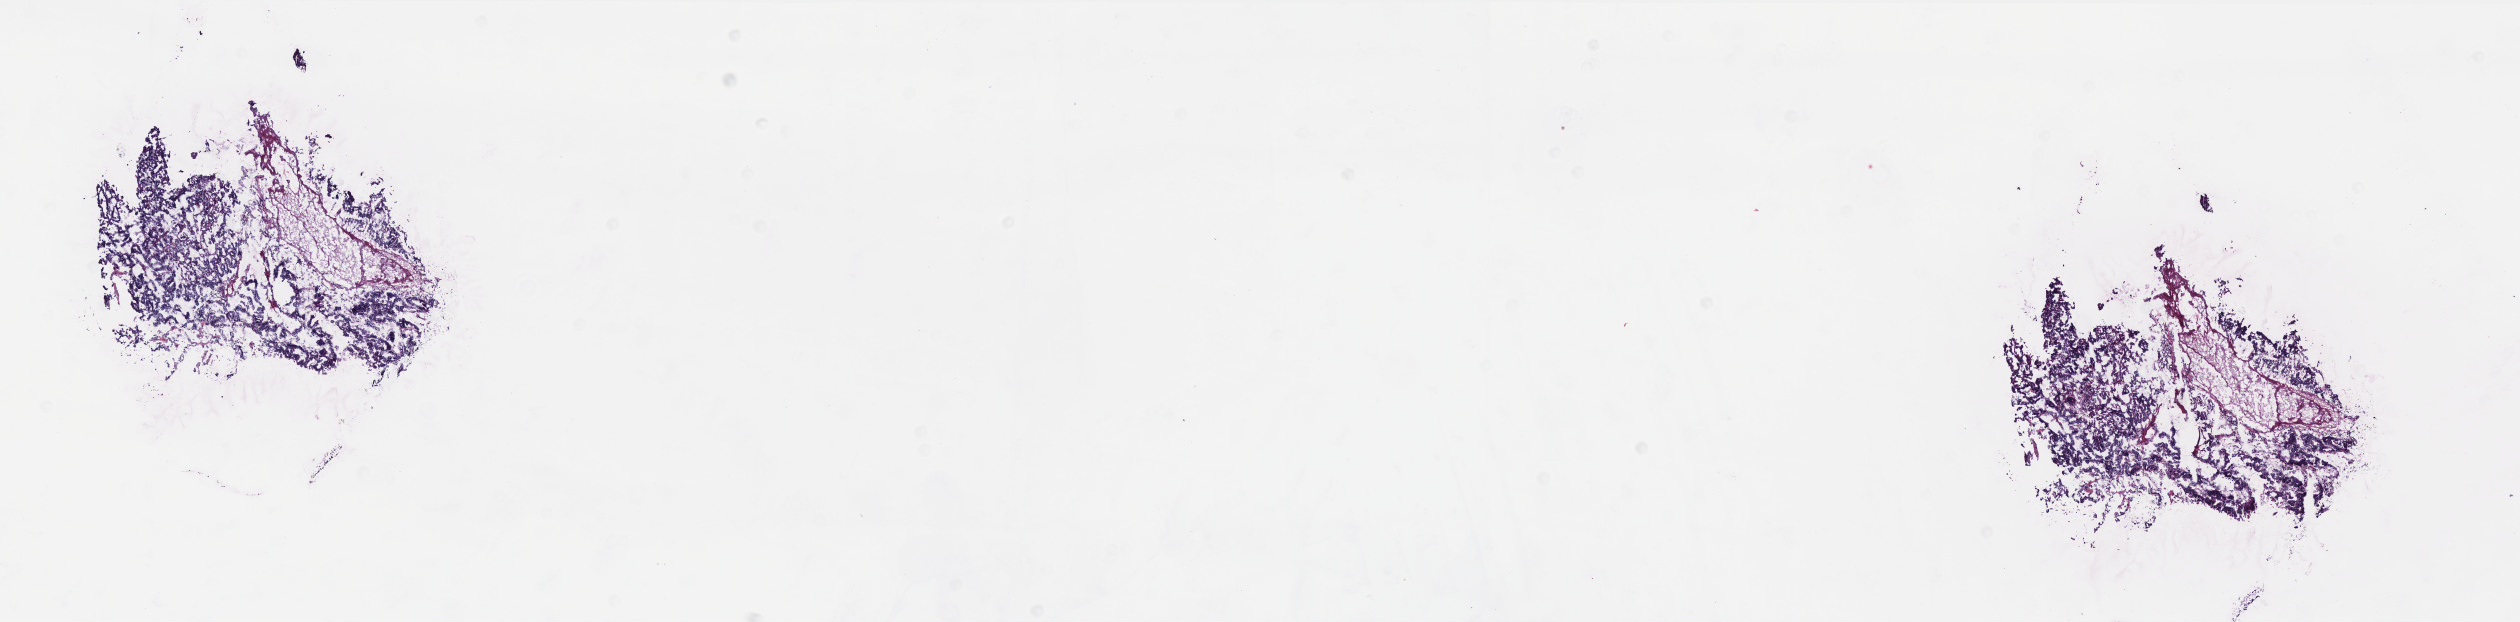
Digitized H&E-stained tissue section (whole slide) — whole scanned area (about 20.2 x 5.0 mm) shown as a low-resolution overview, frozen section from the bottom of the tissue portion, primary tumour sample from the uterus. Patient: female, age at initial diagnosis 63 years. Histologic grade: G2 (moderately differentiated). Pathologist review of this section (percent, as recorded): tumour cells 100%, tumour nuclei 80%, normal cells 0%, stromal cells 0%, necrosis 0%. Infiltration values recorded for this section: lymphocyte infiltration 0%, monocyte infiltration 0%, neutrophil infiltration 0%.
FIGO stage: IA. Pathologic diagnosis: Endometrioid adenocarcinoma, NOS (endometrium). Lymph nodes positive (case pathology): 0 of 14 examined.